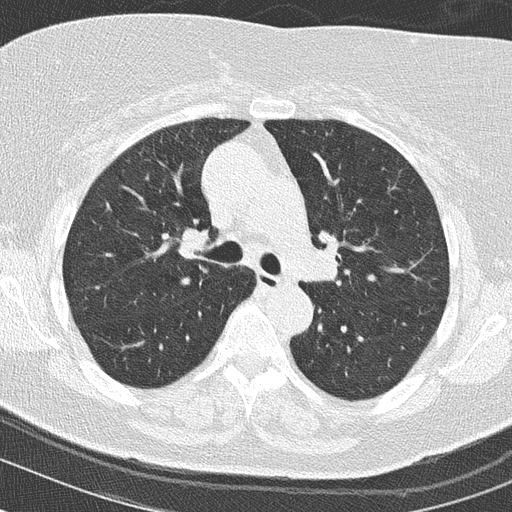
Low-dose screening chest CT, axial slice, baseline annual screen, lung window (W 1500 / L -600 HU), lung (sharp) reconstruction kernel (B50f), slice 49 of 149 in the series. Female, age 63 years at enrolment.
Lesion marked by an expert reader, box from (x=159, y=218) to (x=226, y=271) px. Screening reader's record for this exam: no non-calcified nodule ≥4 mm recorded. Official screen result: negative screen, minor abnormalities not suspicious for lung cancer. Lung cancer was diagnosed 149 days after this screen: squamous cell carcinoma, keratinizing, NOS, right upper lobe, moderately differentiated (G2), stage IIA (AJCC 6th edition), 42 mm at pathology.